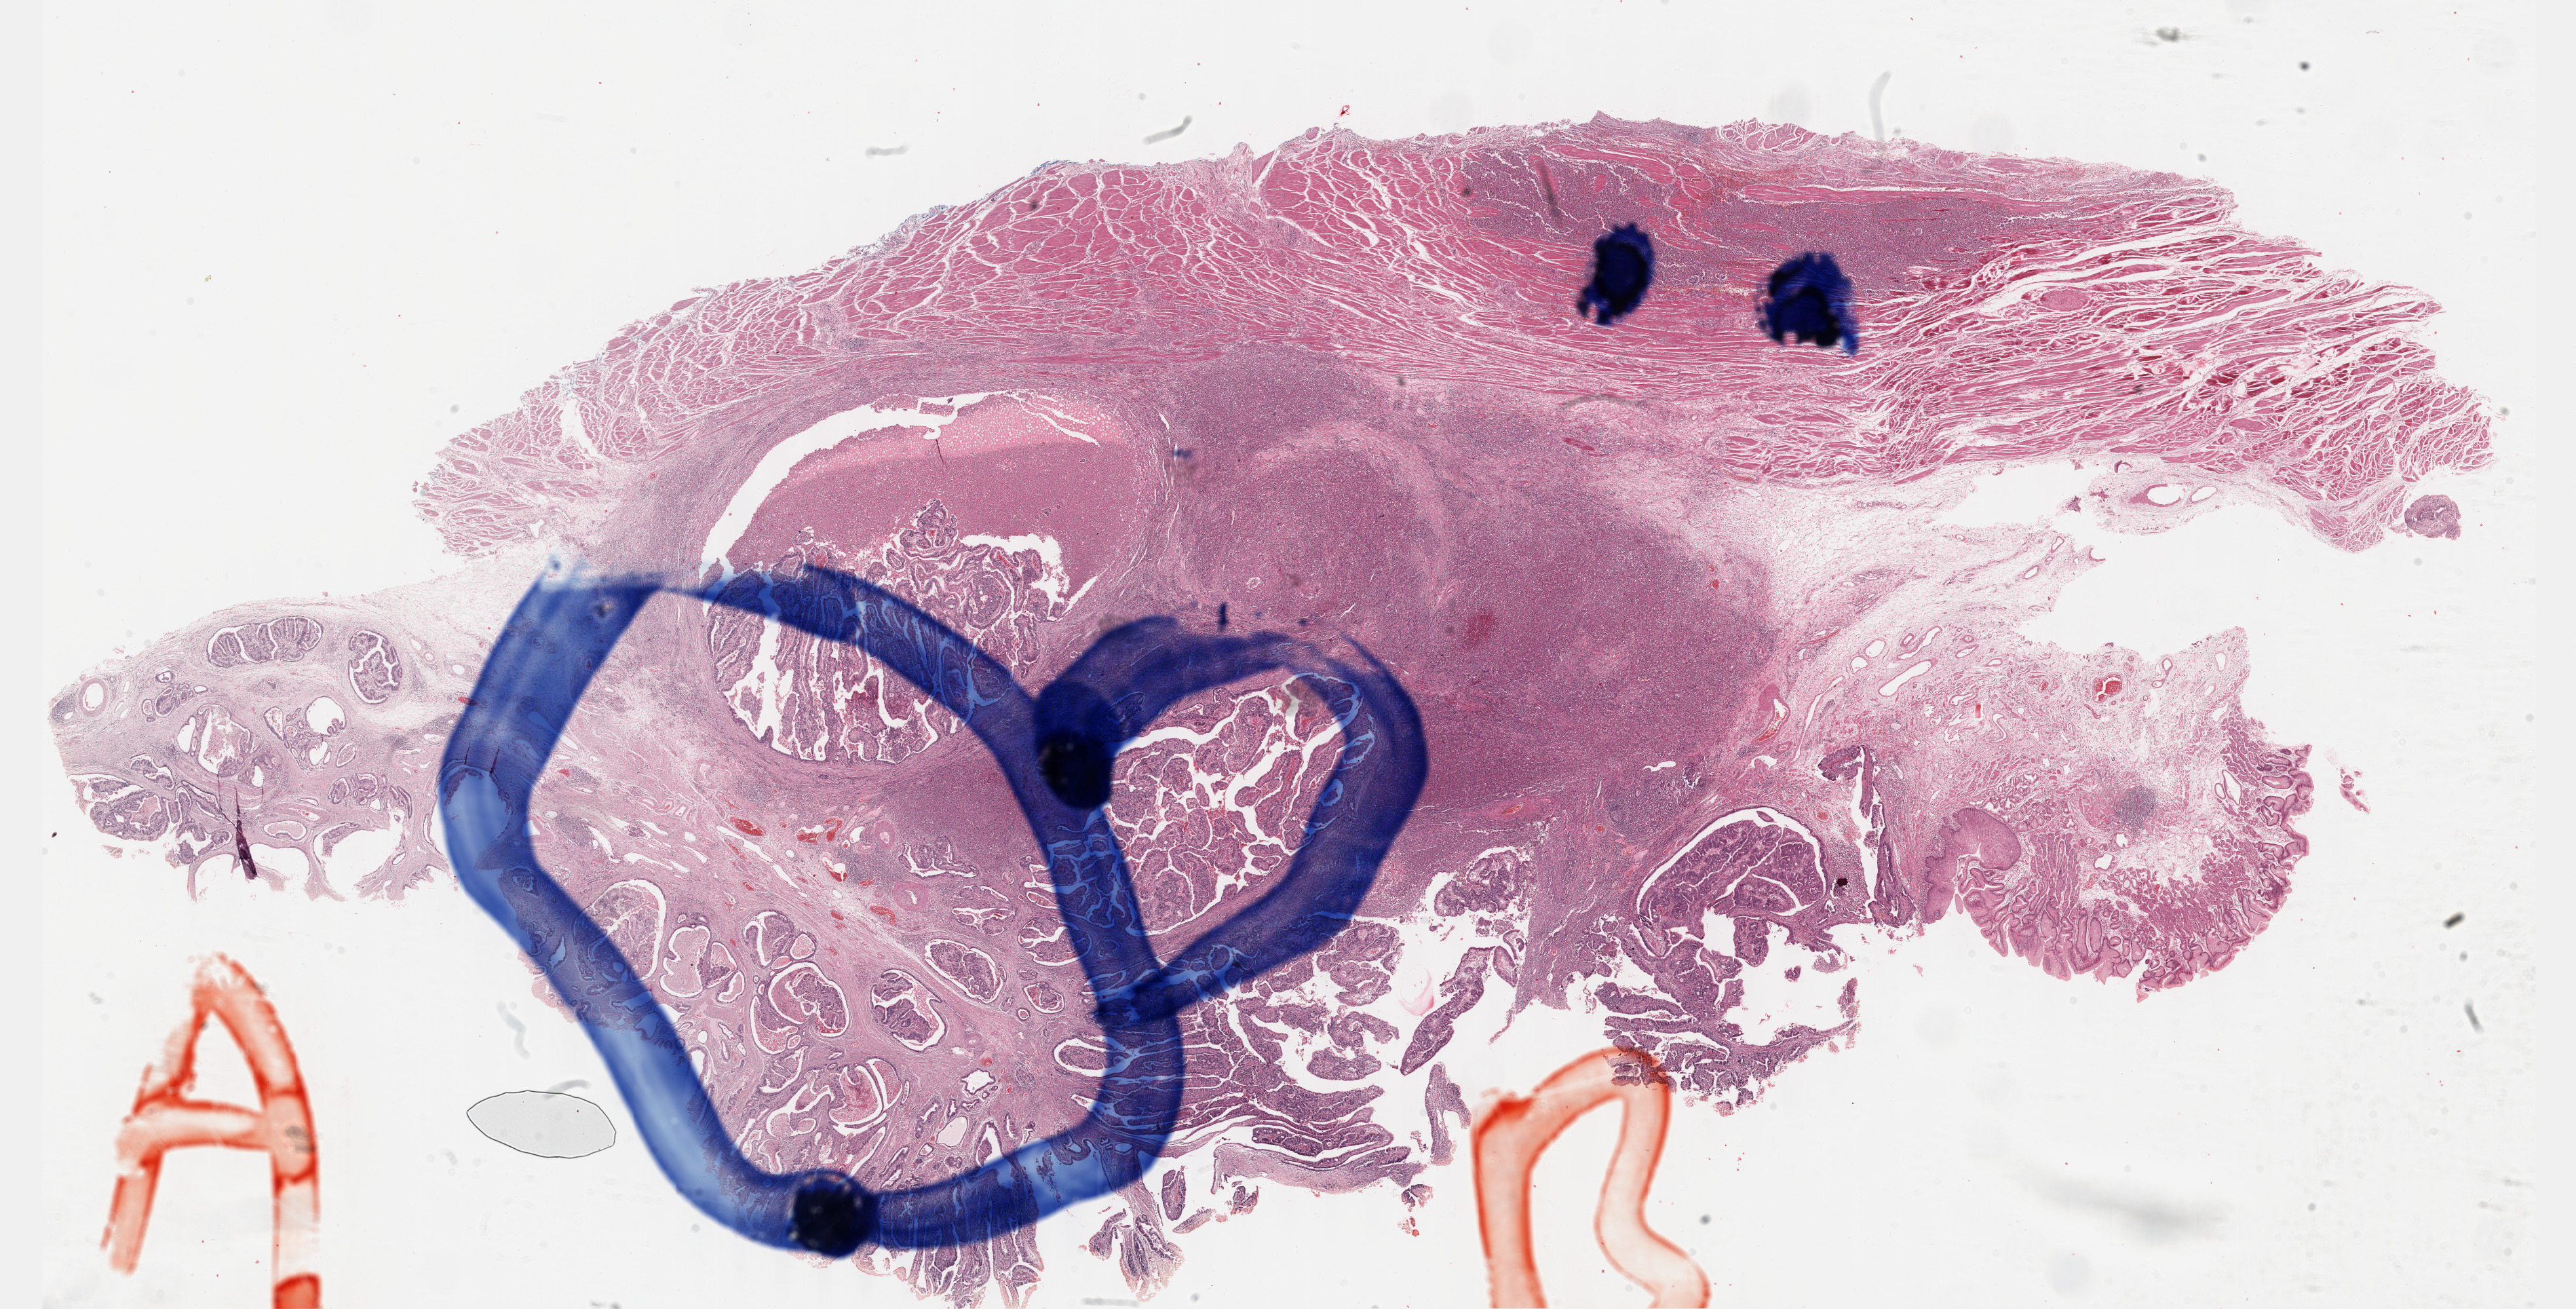
Digitized H&E tissue section (whole slide), low-resolution overview of the scanned area, about 30.7 x 15.6 mm (from a 40x scan), formalin-fixed paraffin-embedded (FFPE) diagnostic section, primary tumour sample from the esophagus. Male patient; age at initial diagnosis 53 years. Histologic grade: G2 (moderately differentiated).
Diagnosis: Adenocarcinoma, NOS (lower third of esophagus). AJCC pathologic stage: IIB (5th edition).